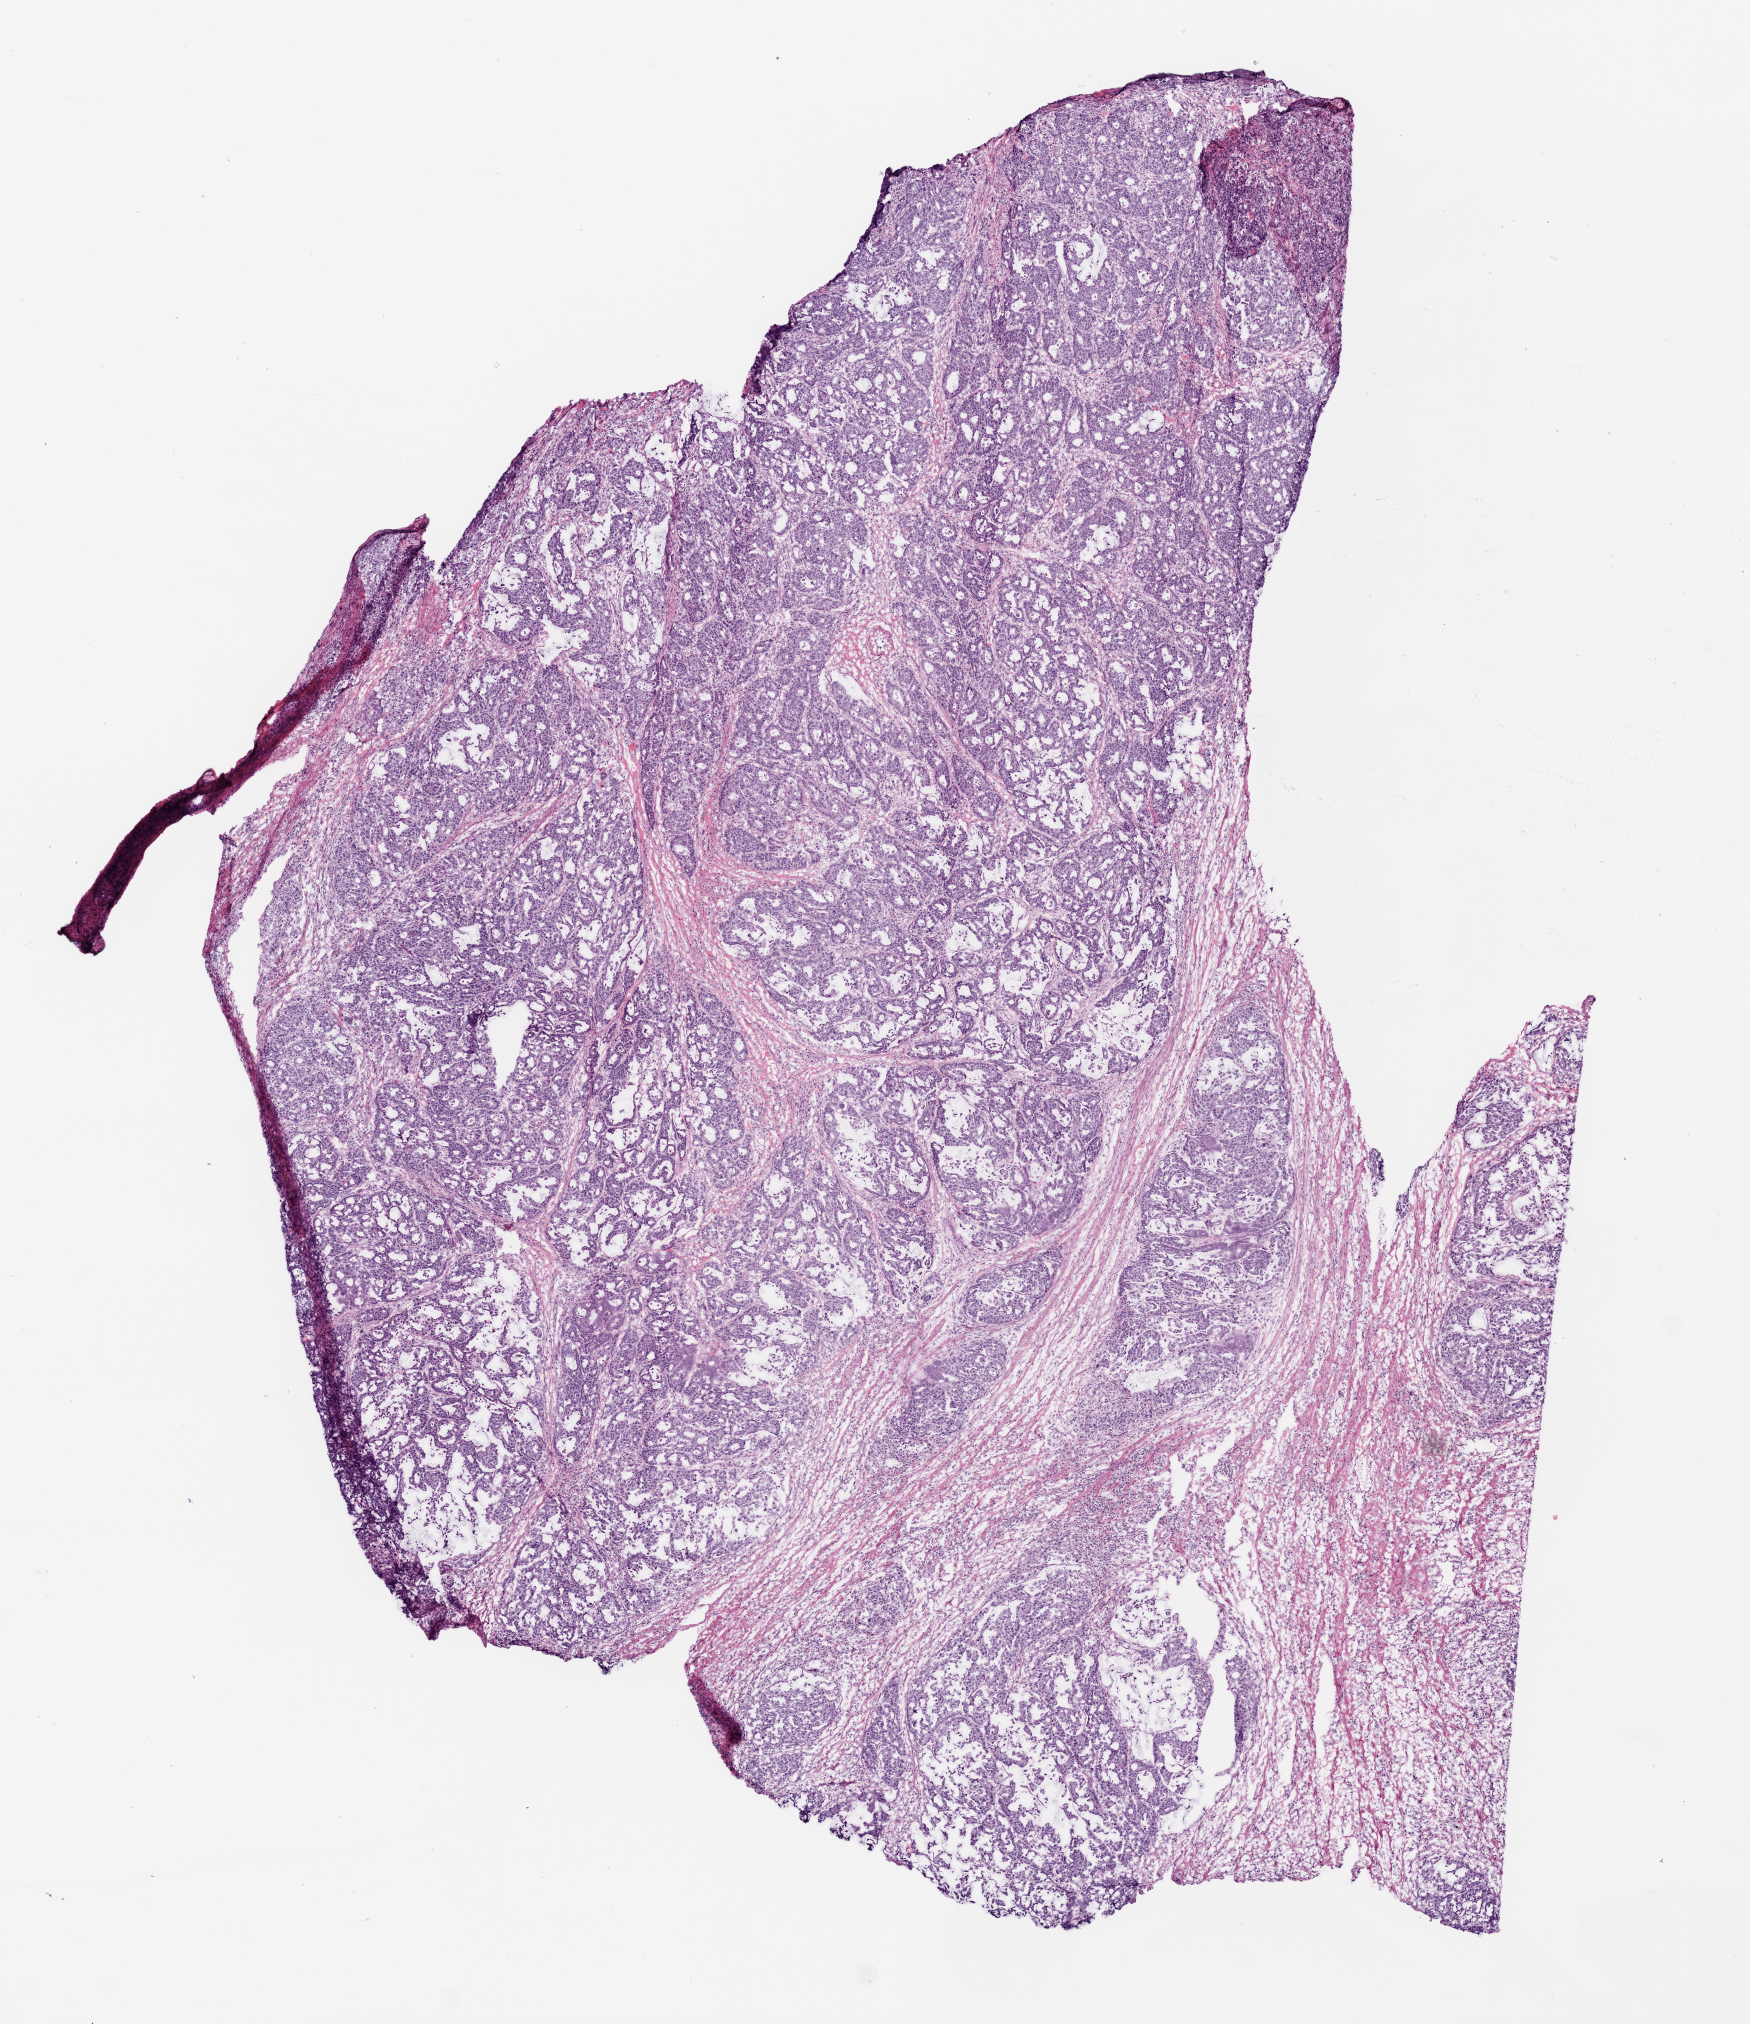
Hematoxylin and eosin (H&E) stained whole-slide image, shown as a low-resolution overview of the whole scanned area (about 7.0 x 8.1 mm), frozen section from the top of the tissue portion, colon, primary tumour sample. Female, age 89 years at initial diagnosis. Pathologist review of this section (percent, as recorded): tumour cells 80%, tumour nuclei 80%, normal cells 0%, stromal cells 20%, necrosis 0%.
Histologic diagnosis: Mucinous adenocarcinoma. AJCC pathologic stage: IIA.